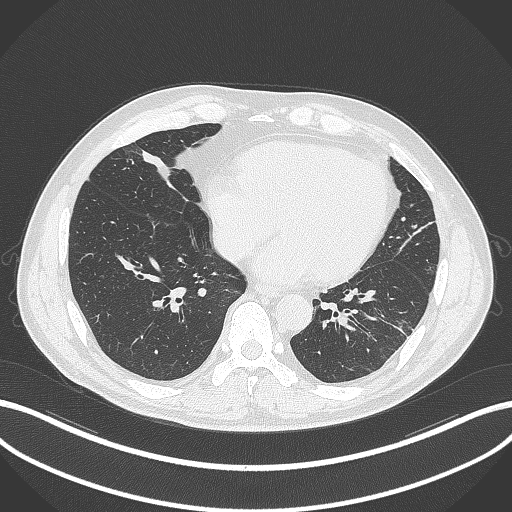
Chest CT, one axial slice; position 89 of 399 along the scan axis; lung window (W 1500 / L -600 HU); 512 × 512 image matrix. Patient: male, 59 years. From the clinical record (not read from this slice): clinical TNM (as recorded): T2a N1 M0.
Annotated regions visible in this slice (bounding box drawn by a radiologist):
- lung tumour (recorded histology: adenocarcinoma): box from (x=137, y=144) to (x=176, y=190) px